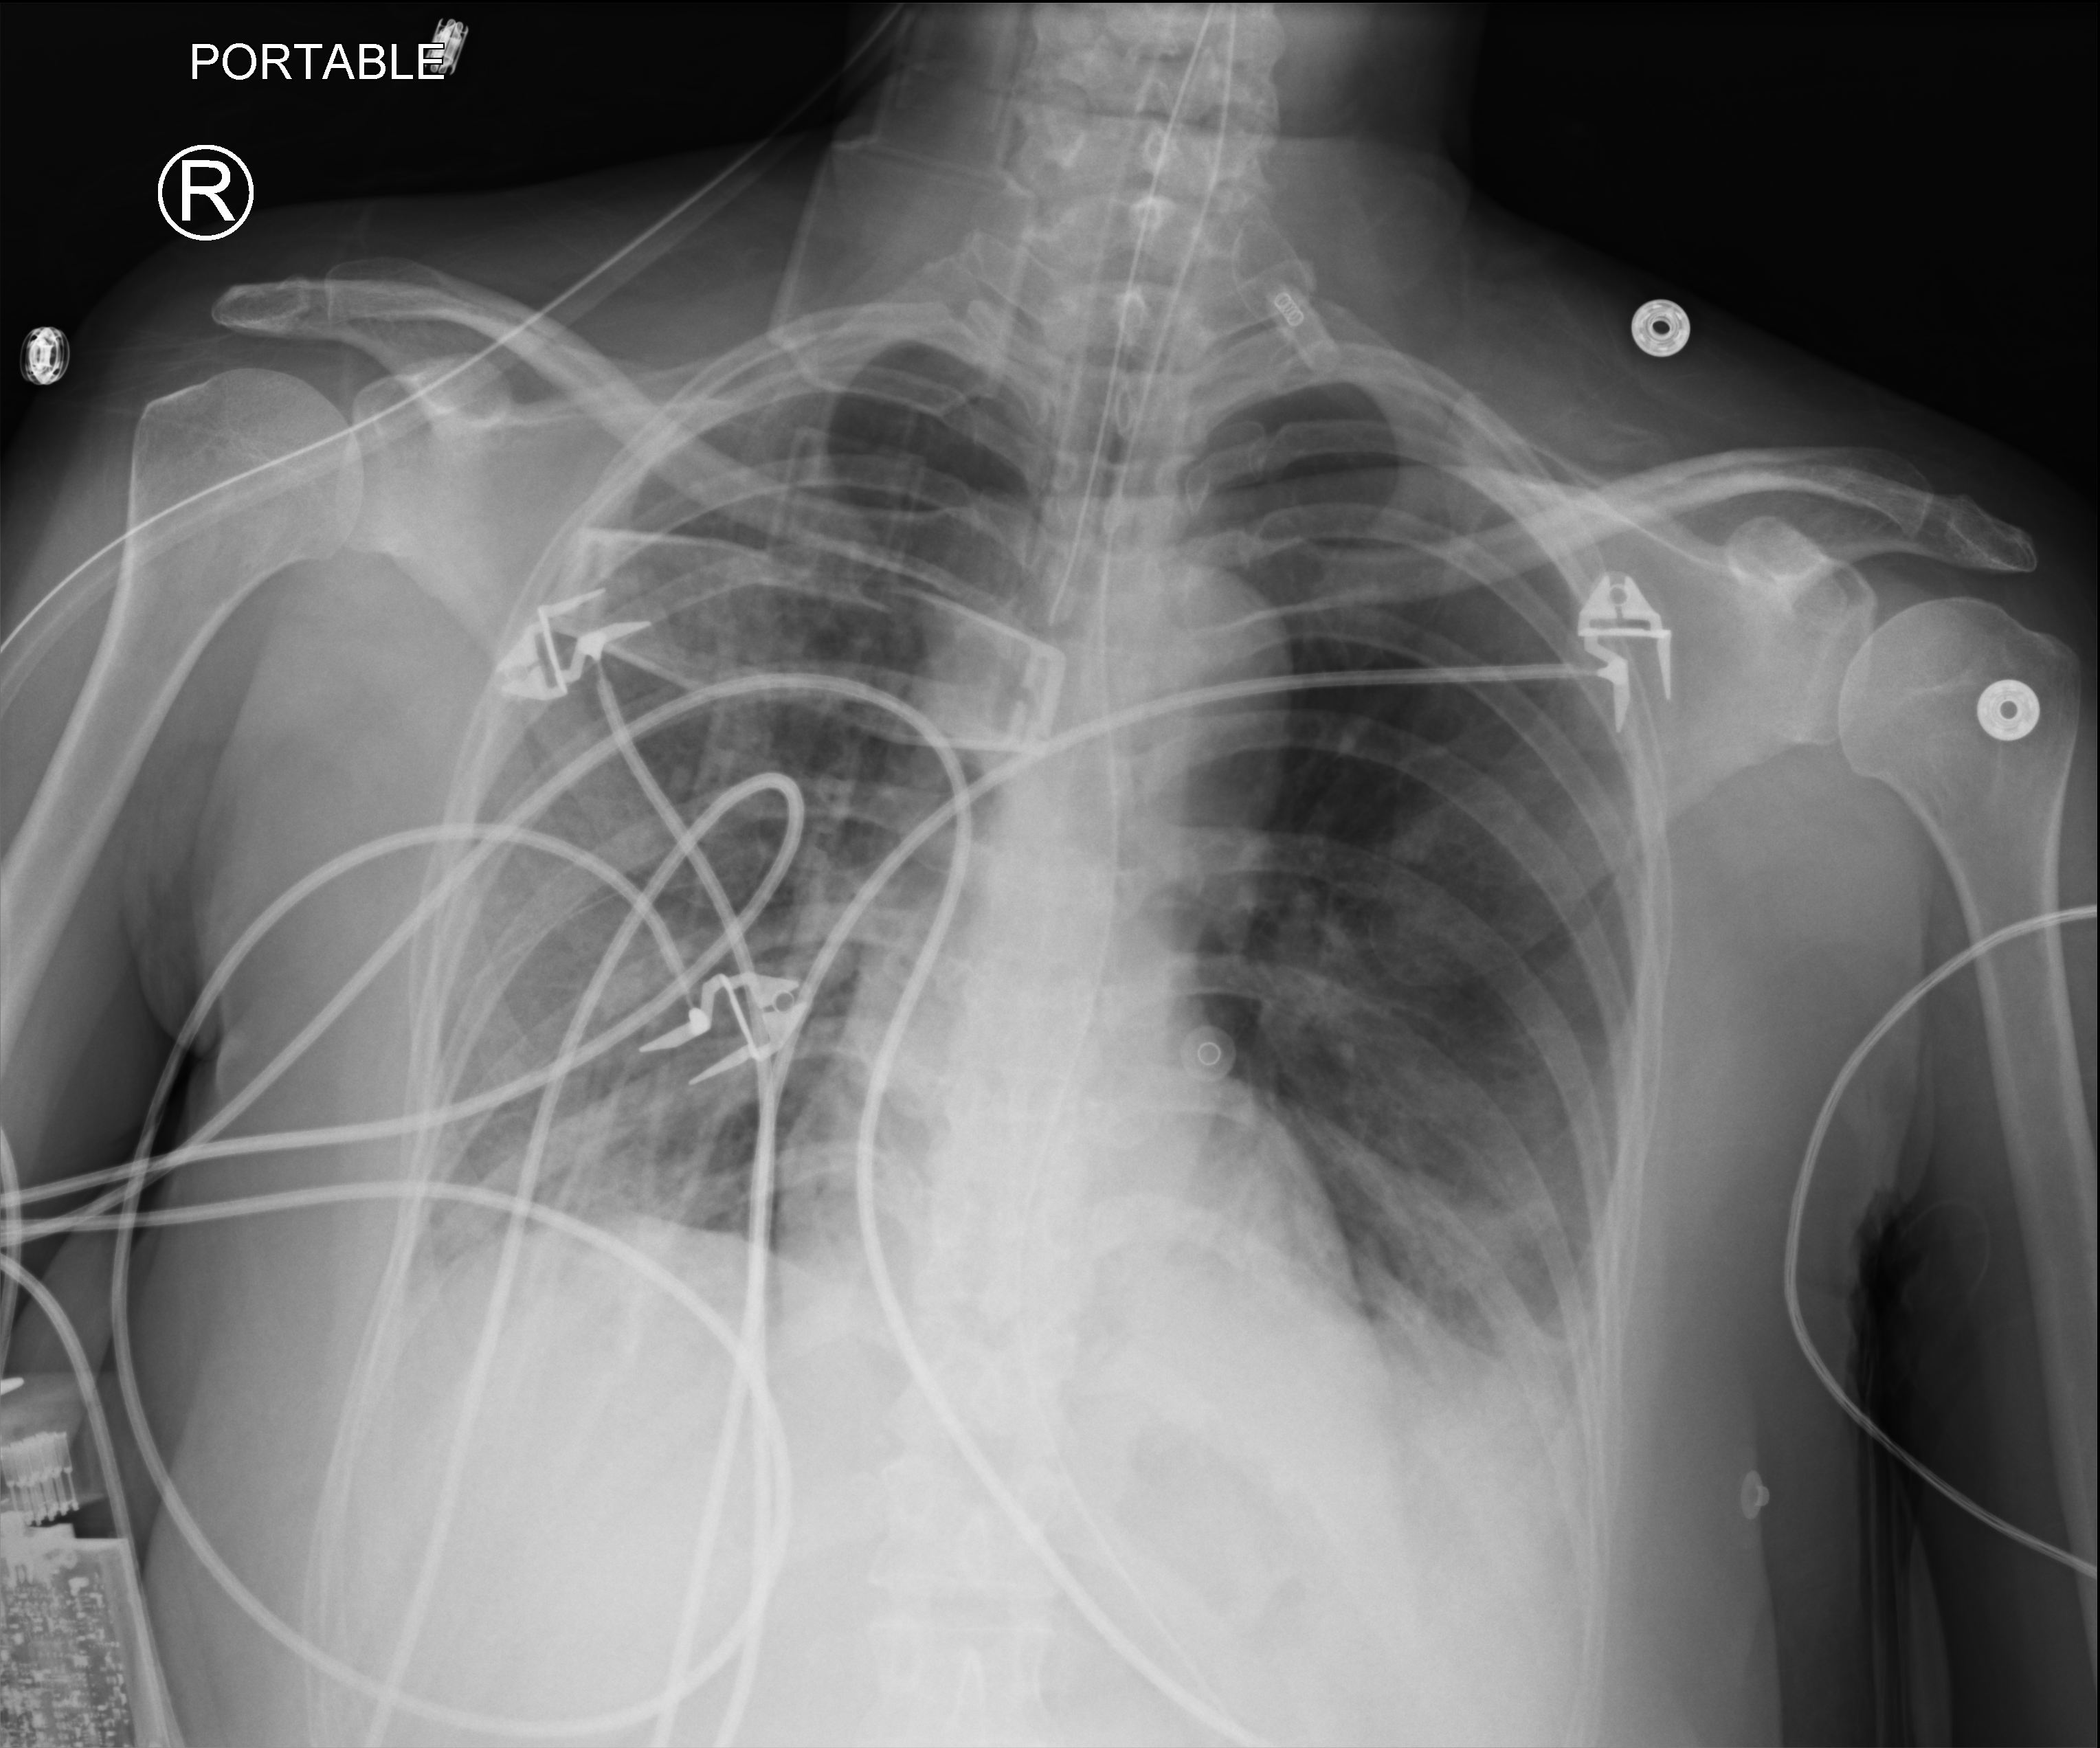
Bedside chest radiograph (computed radiography). Patient hospitalised with COVID-19; female, aged 18–59 years.
Admission-level facts for this patient (not findings on this image; timing relative to this image not recorded):
- hypertension (admission record): yes
- length of hospital stay: 16 days